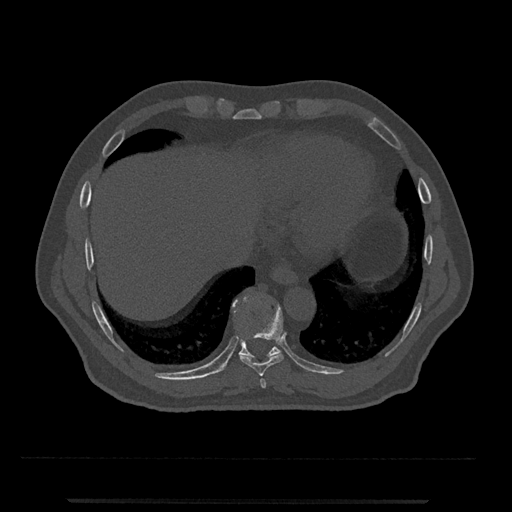
CT including the spine, one axial slice; slice 552 of 797 in the series (ordered by position); reconstruction kernel Br40s/3; 120 kVp; bone window (W 1800 / L 400 HU); 0.5 mm slice thickness; 512 × 512 image matrix, field of view 419 × 419 mm. Male patient, age 63 years. From the clinical record (not read from this slice): primary cancer: prostate.
Annotated regions visible in this slice (semi-automatic segmentation, software-assisted and operator-edited):
- T10 vertebra: bounding box <222,295,281,371> (left, top, right, bottom; pixels)
- T8 vertebra: <260,379,267,388>
- T9 vertebra: <240,305,284,376>